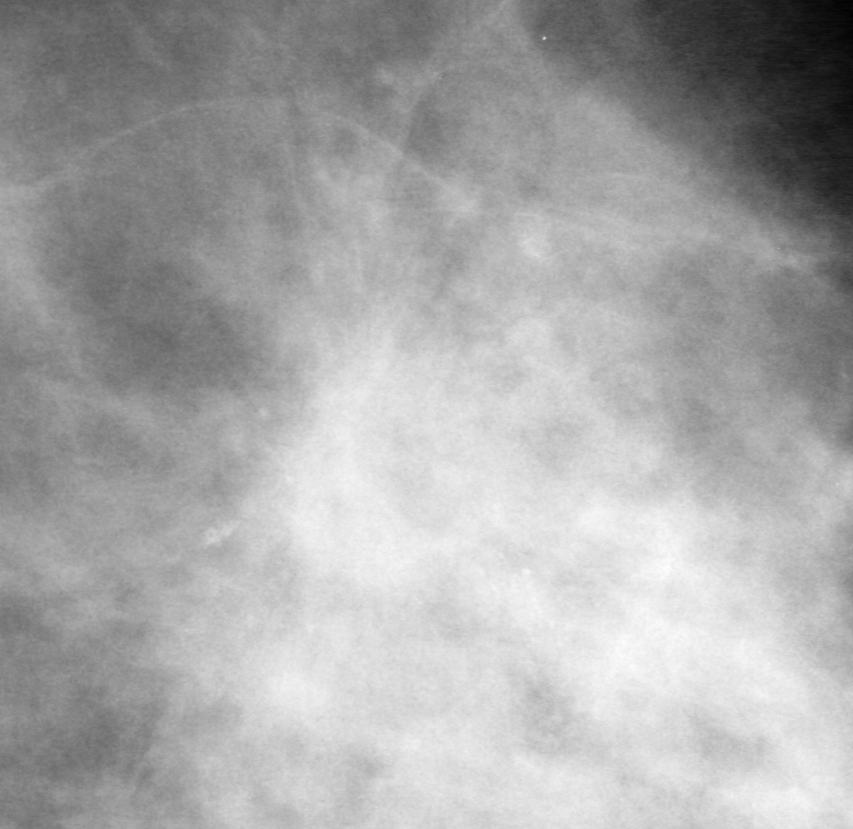
Region of interest cut from a scanned film mammogram (one marked finding); left breast; MLO view.
Marked abnormality: calcifications, morphology amorphous, distribution clustered; BI-RADS assessment category 3; pathology result (as recorded, not read from the image): malignant.